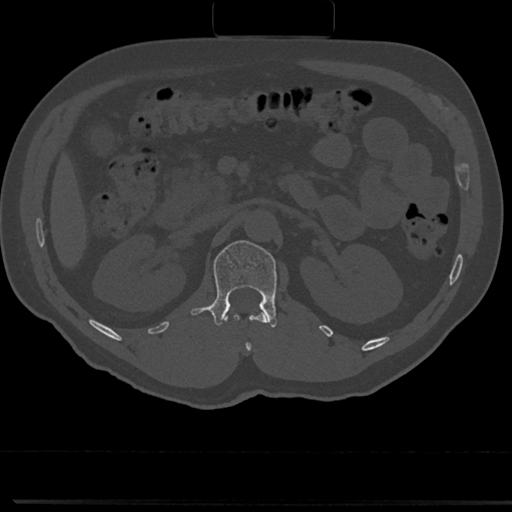
CT including the spine, one axial slice. Slice 98 of 817 in the series (ordered by position). Bone window (W 1800 / L 400 HU). 0.5 mm slice thickness. 512 × 512 image matrix, field of view 355 × 355 mm. Male patient, age 61 years. From the clinical record (not read from this slice): primary cancer: prostate.
Outlined on this slice (semi-automatic segmentation, software-assisted and operator-edited):
- L1 vertebra: bounding box [x1, y1, x2, y2] px = [191, 240, 278, 327]
- T12 vertebra: [247, 313, 267, 349]